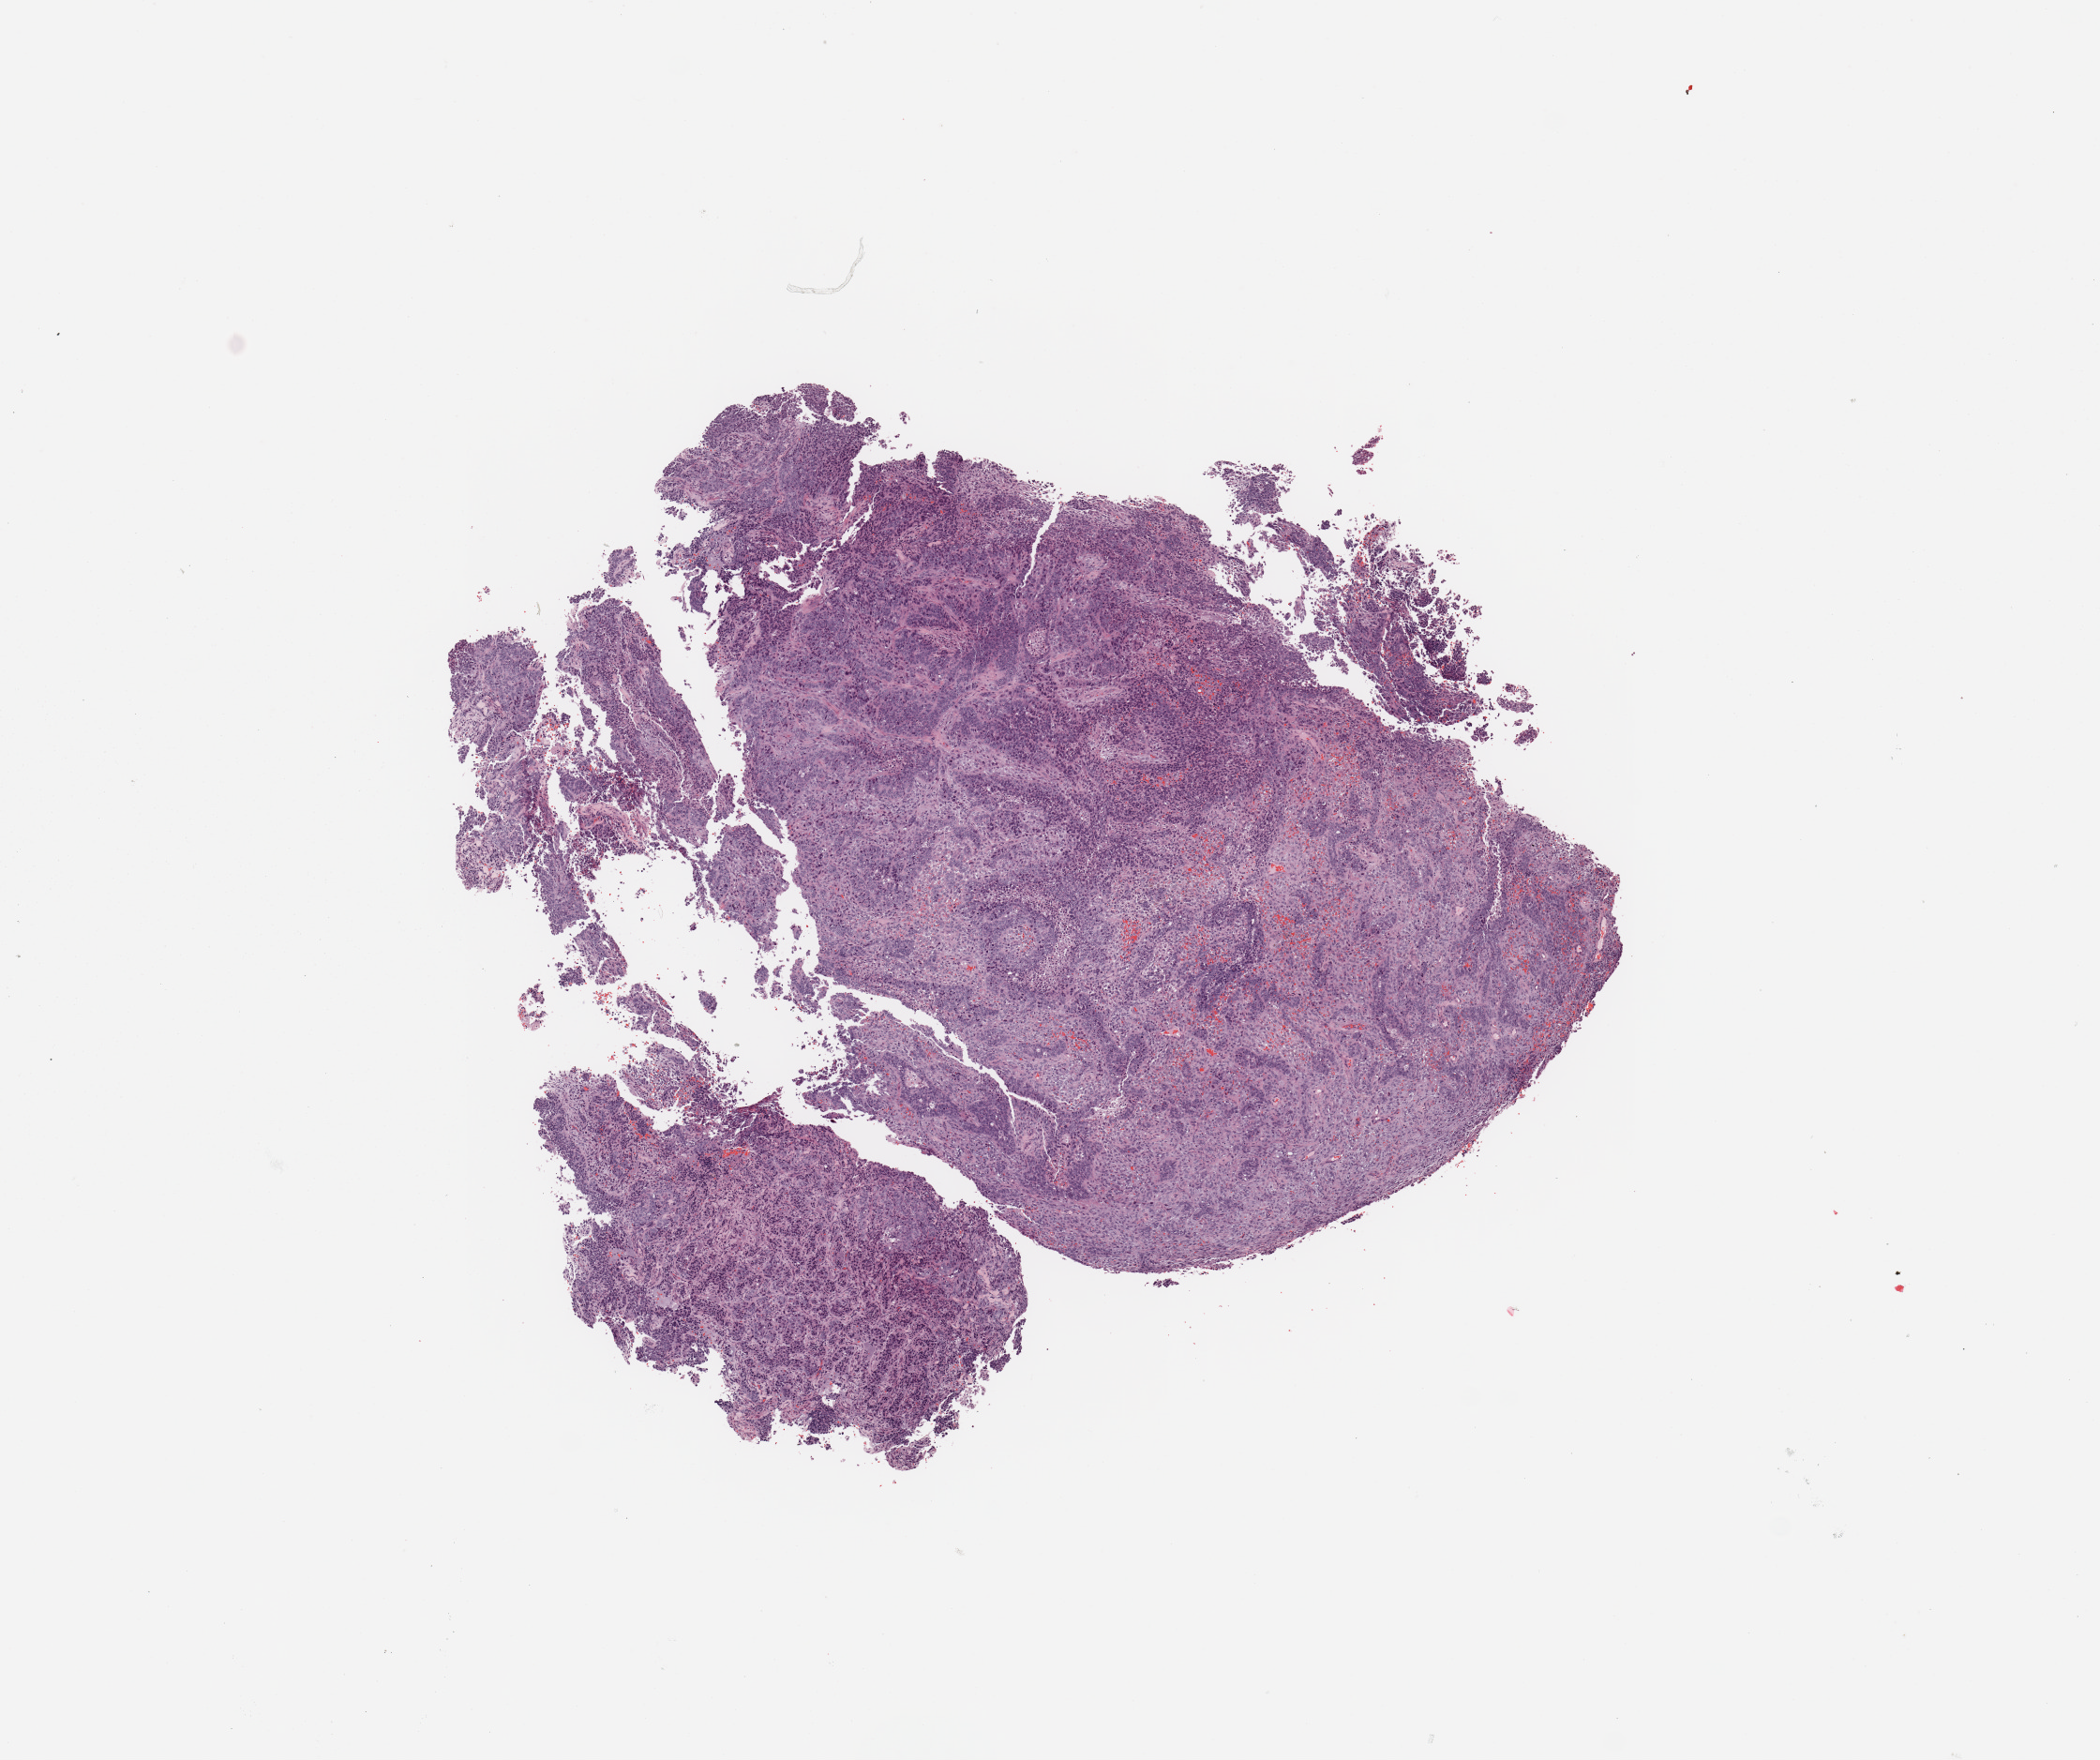
Hematoxylin and eosin (H&E) stained whole-slide image, a low-resolution overview of the entire scanned area, about 8.9 x 7.4 mm, uterus, tumour tissue. Female, 68 y/o. Histologic grade: G3 (poorly differentiated).
Diagnosis: Endometrioid adenocarcinoma, NOS. AJCC pathologic stage: III.